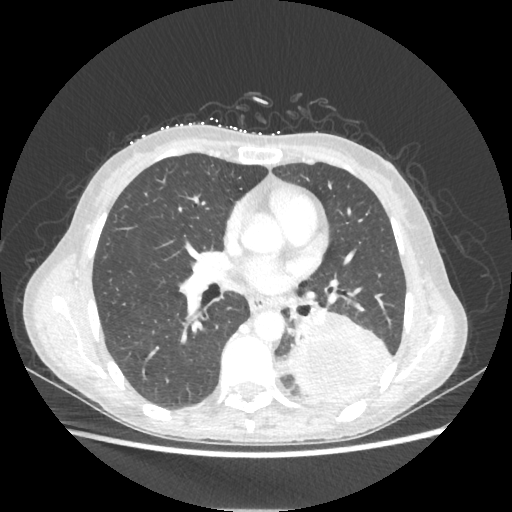
Chest CT, one axial slice; position 113 of 221 along the scan axis; reconstruction kernel STANDARD; 80 kVp; lung window (W 1500 / L -600 HU); 512 × 512 image matrix. Patient: female, 53 years. From the clinical record (not read from this slice): clinical TNM (as recorded): T3 N0 M0.
Annotated regions visible in this slice (rectangle marked by the reading radiologist):
- lung tumour (recorded histology: adenocarcinoma): bounding box (x1, y1, x2, y2) in pixels: (290, 310, 391, 404)